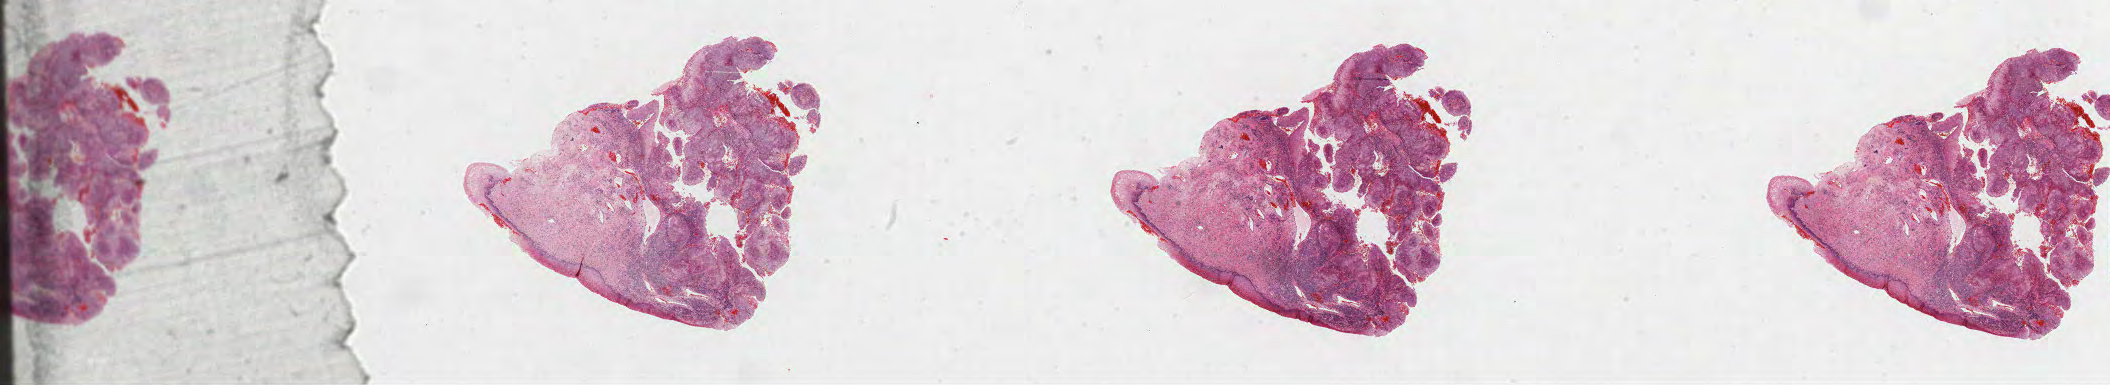
H&E whole-slide image, low-resolution overview of the scanned area, about 34.0 x 6.2 mm. FFPE section. Cervix, primary tumour sample. Female, age 54 years at initial diagnosis. Histologic grade: G2 (moderately differentiated).
Diagnosis: Squamous cell carcinoma, large cell, nonkeratinizing, NOS (cervix uteri). FIGO stage: IIIB.